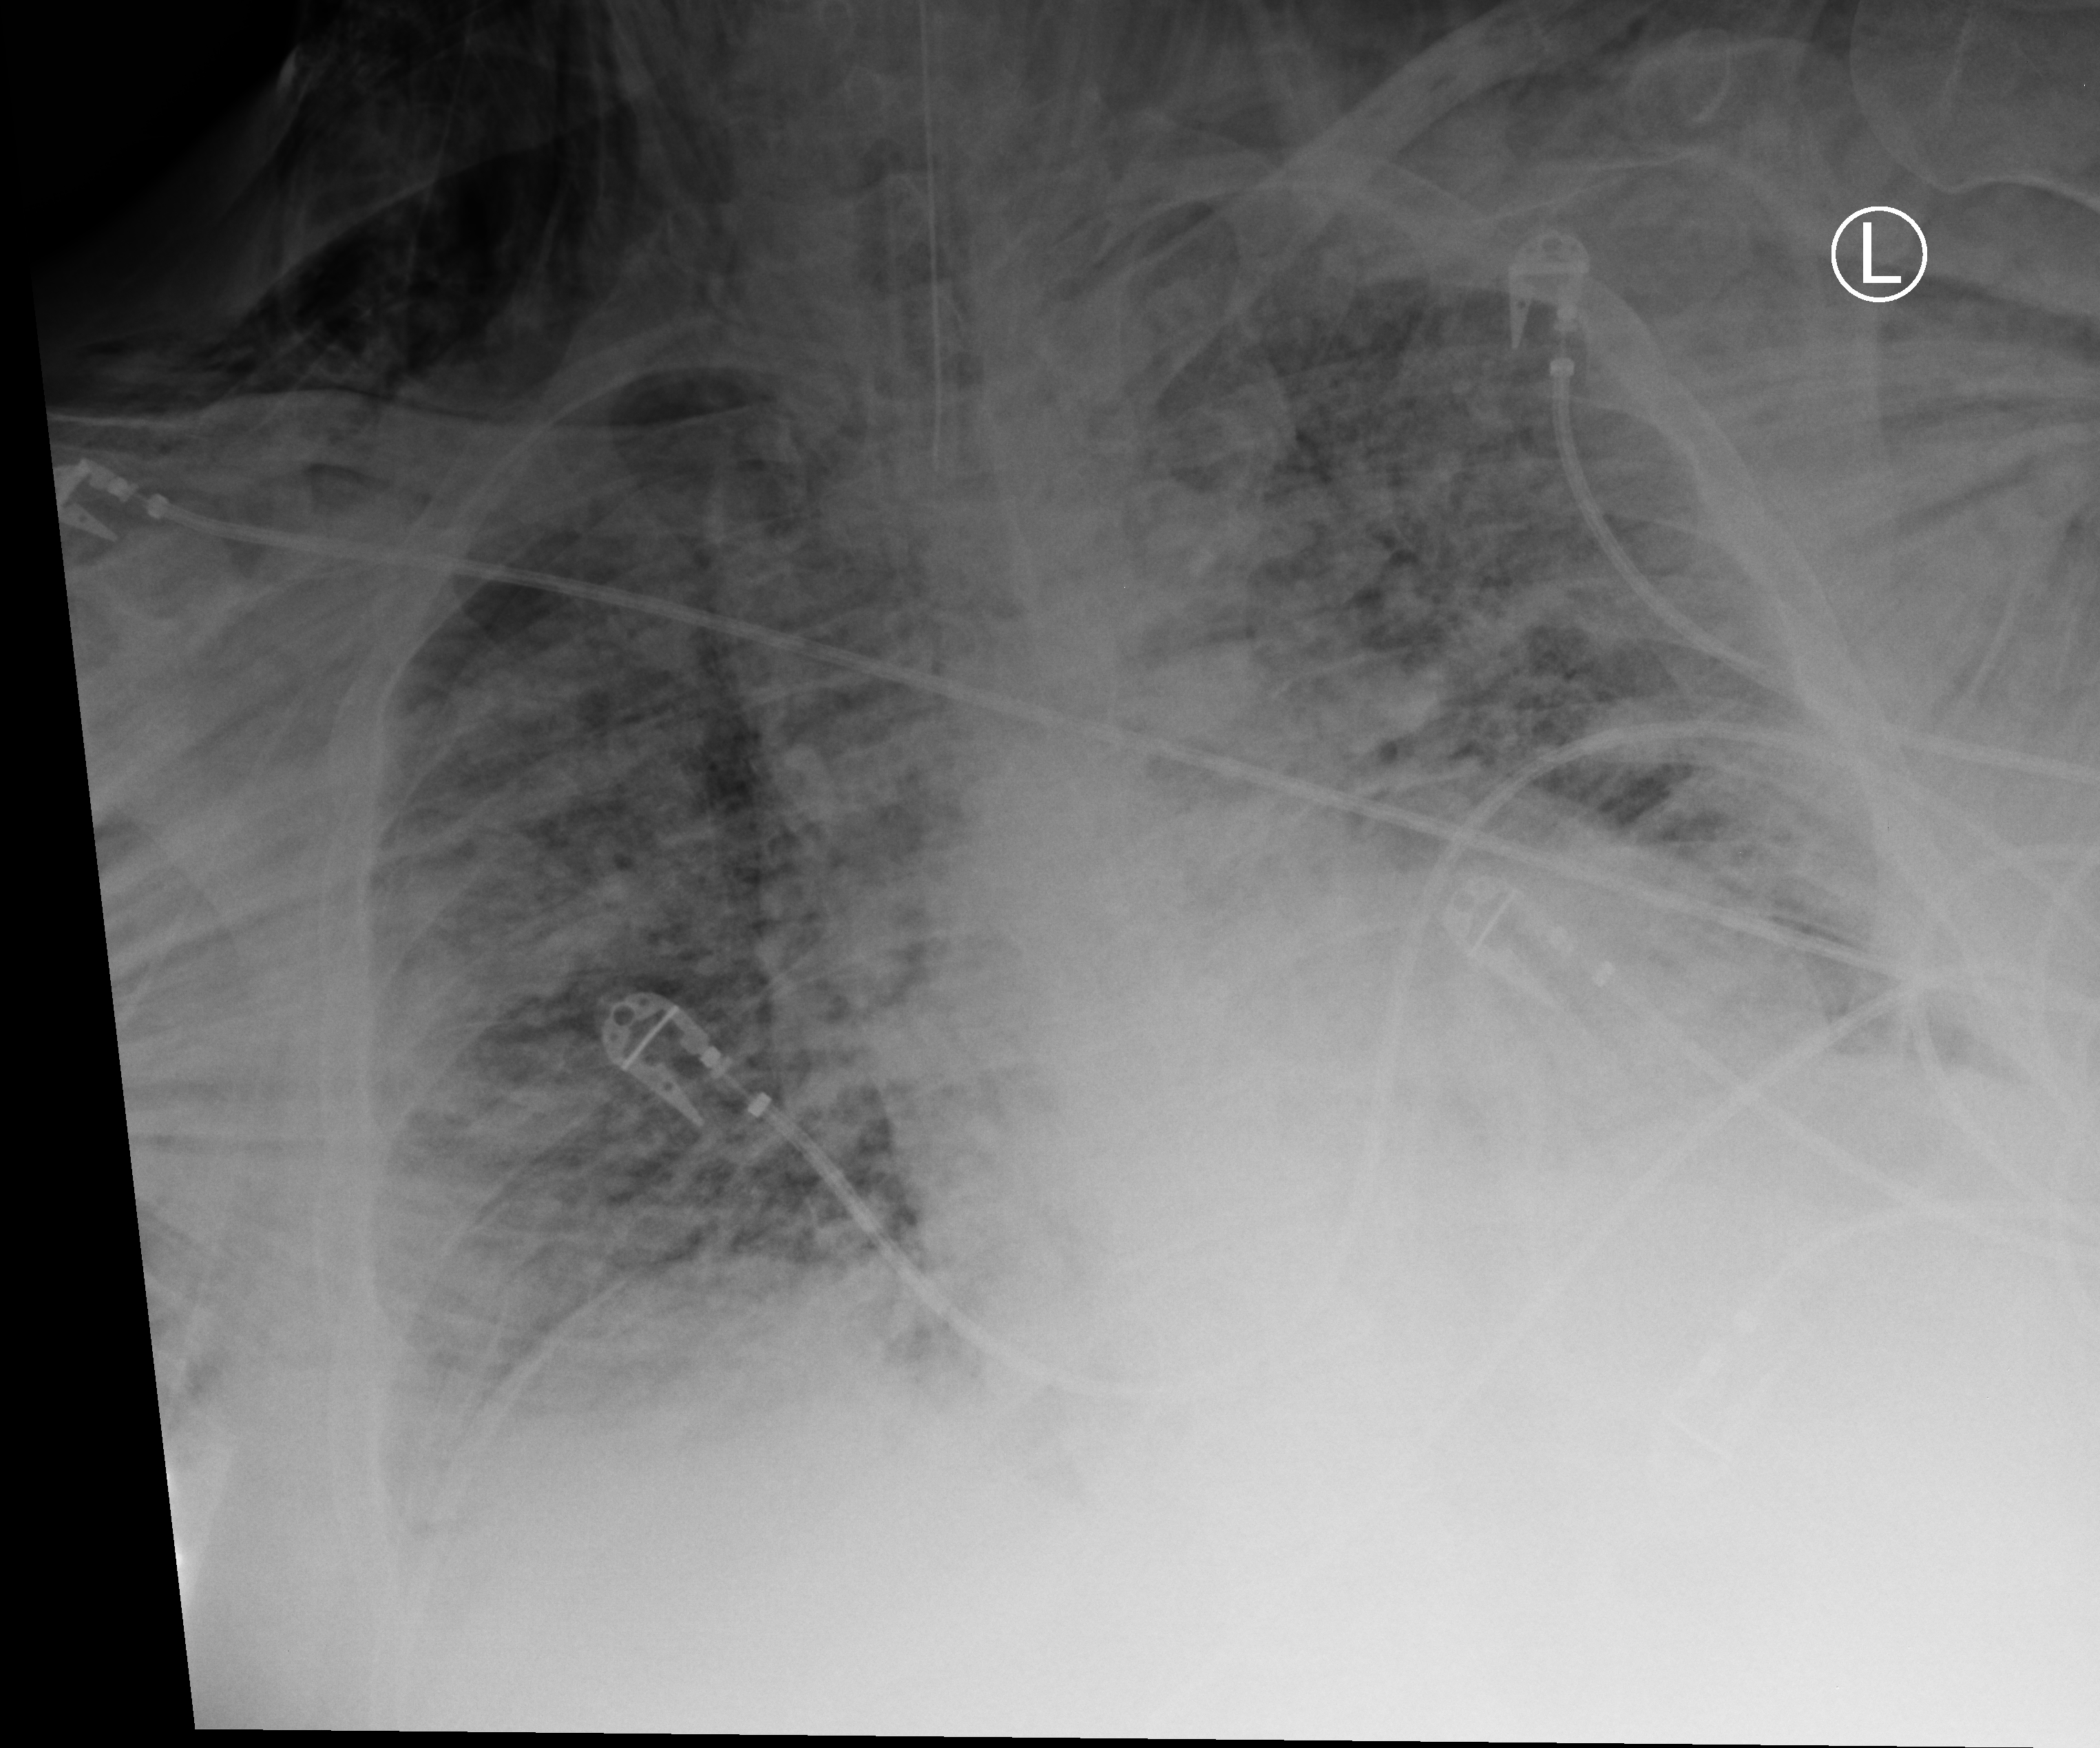
Chest X-ray (portable), anteroposterior (AP) projection. Patient hospitalised with COVID-19, aged 18–59 years.
Admission-level facts for this patient (not findings on this image; timing relative to this image not recorded): admitted to intensive care during this hospital stay: yes; chronic kidney disease (admission record): no.